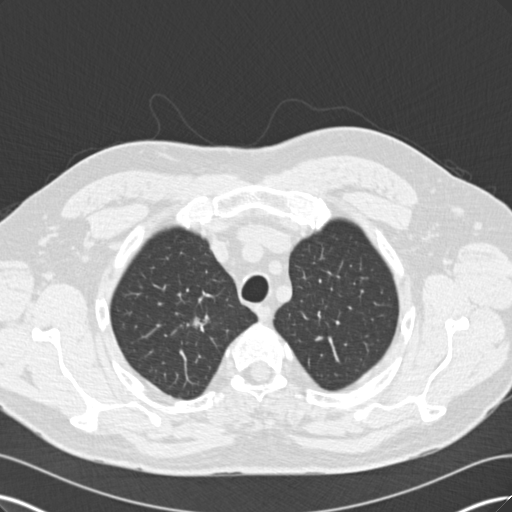
Low-dose screening chest CT, one axial slice; position 145 of 171 along the scan axis; reconstruction kernel B30f; 120 kVp; lung window (W 1500 / L -600 HU); 512 × 512 image matrix, field of view 360 × 360 mm.
Annotated regions visible in this slice (manually delineated by an expert):
- lesion 1 (tumor, upper lobe of right lung): box from (x=187, y=315) to (x=212, y=339) px